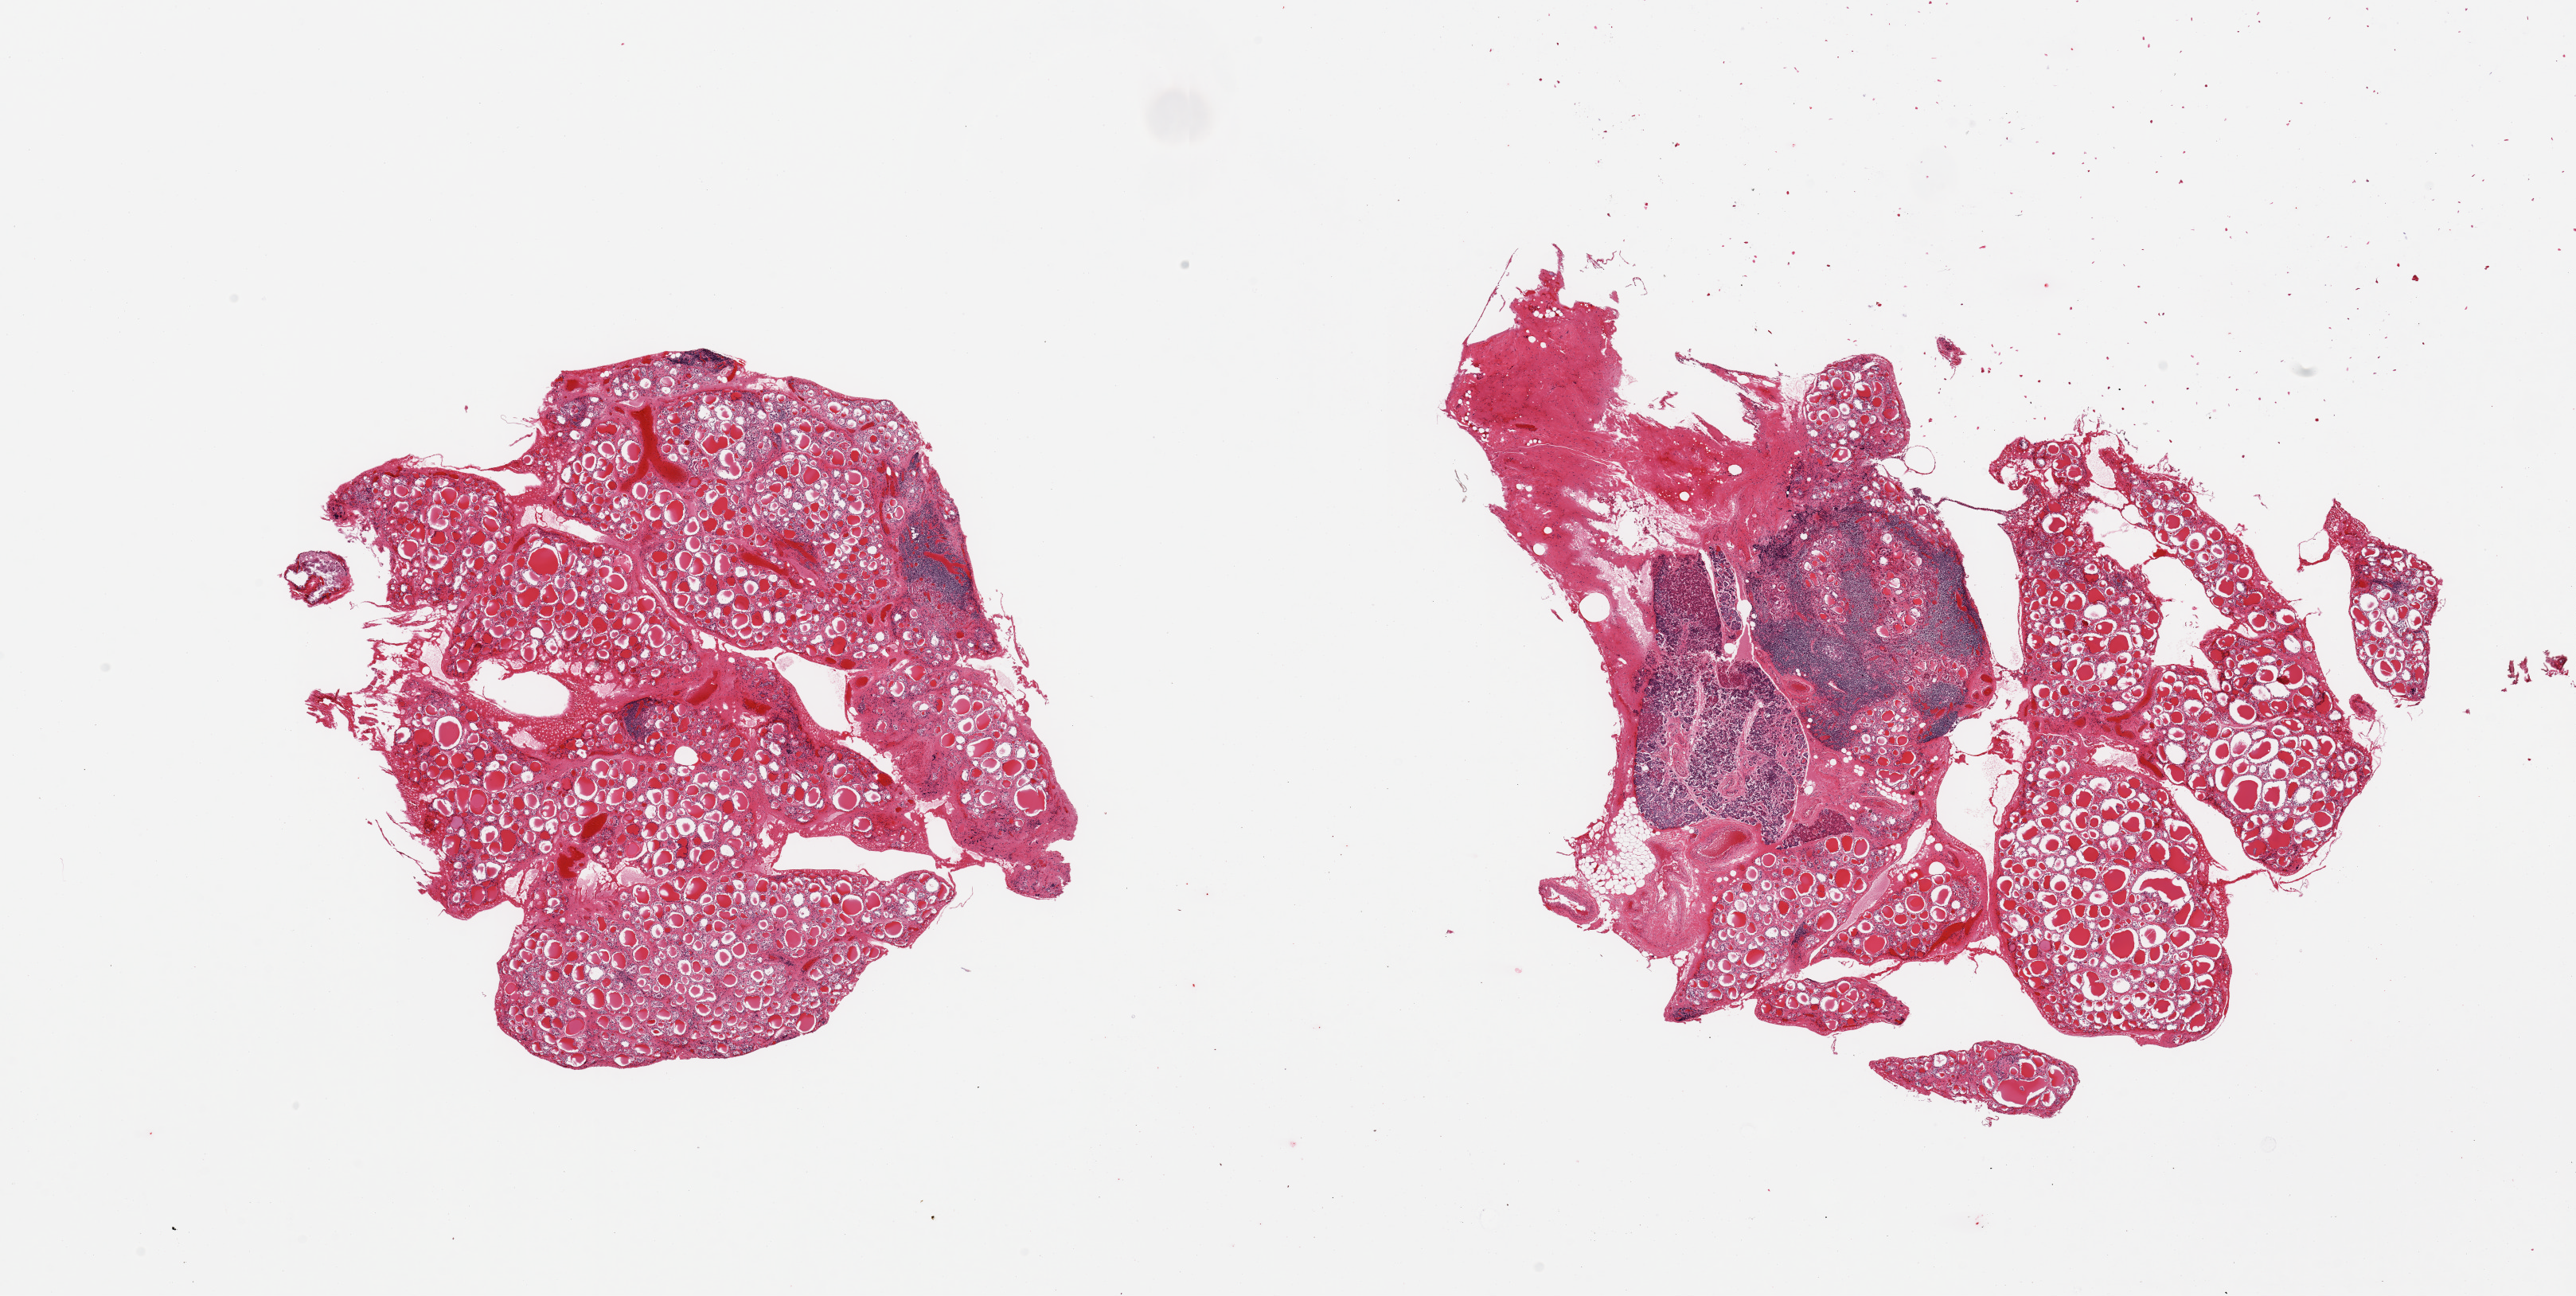
Whole-slide image, H&E stain, brightfield, low-resolution overview of the scanned area, about 25.6 x 12.9 mm (slide scanned at 20x); PAXgene-fixed, paraffin-embedded tissue; target tissue: thyroid; donor tissue sample. Donor: female.
Pathologist's review note for this sample: 2 pieces: 1 has a 2.6x1.7 mm parathyroid and surrounding stroma; lymphoid collections may represent Hashimoto thyroiditis; Piece with parathyroid has about 50% thyroid tissue.